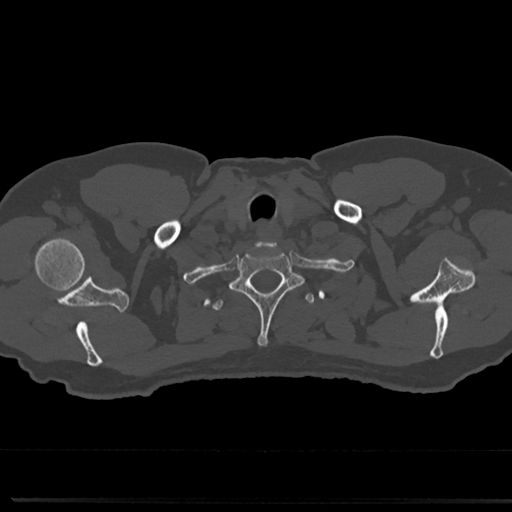
CT including the spine, one axial slice. Position 671 of 817 along the scan axis. Reconstruction kernel Br40s/3. 120 kVp. Bone window (W 1800 / L 400 HU). 0.5 mm slice thickness. 512 × 512 image matrix, field of view 355 × 355 mm. Male patient, age 61 years. Case-level facts recorded for this patient, not image findings: primary cancer: prostate.
Structures marked on this image (semi-automatically segmented with operator editing):
- T1 vertebra: bounding box (x1, y1, x2, y2) in pixels: (232, 248, 299, 346)
- T2 vertebra: (212, 291, 315, 314)